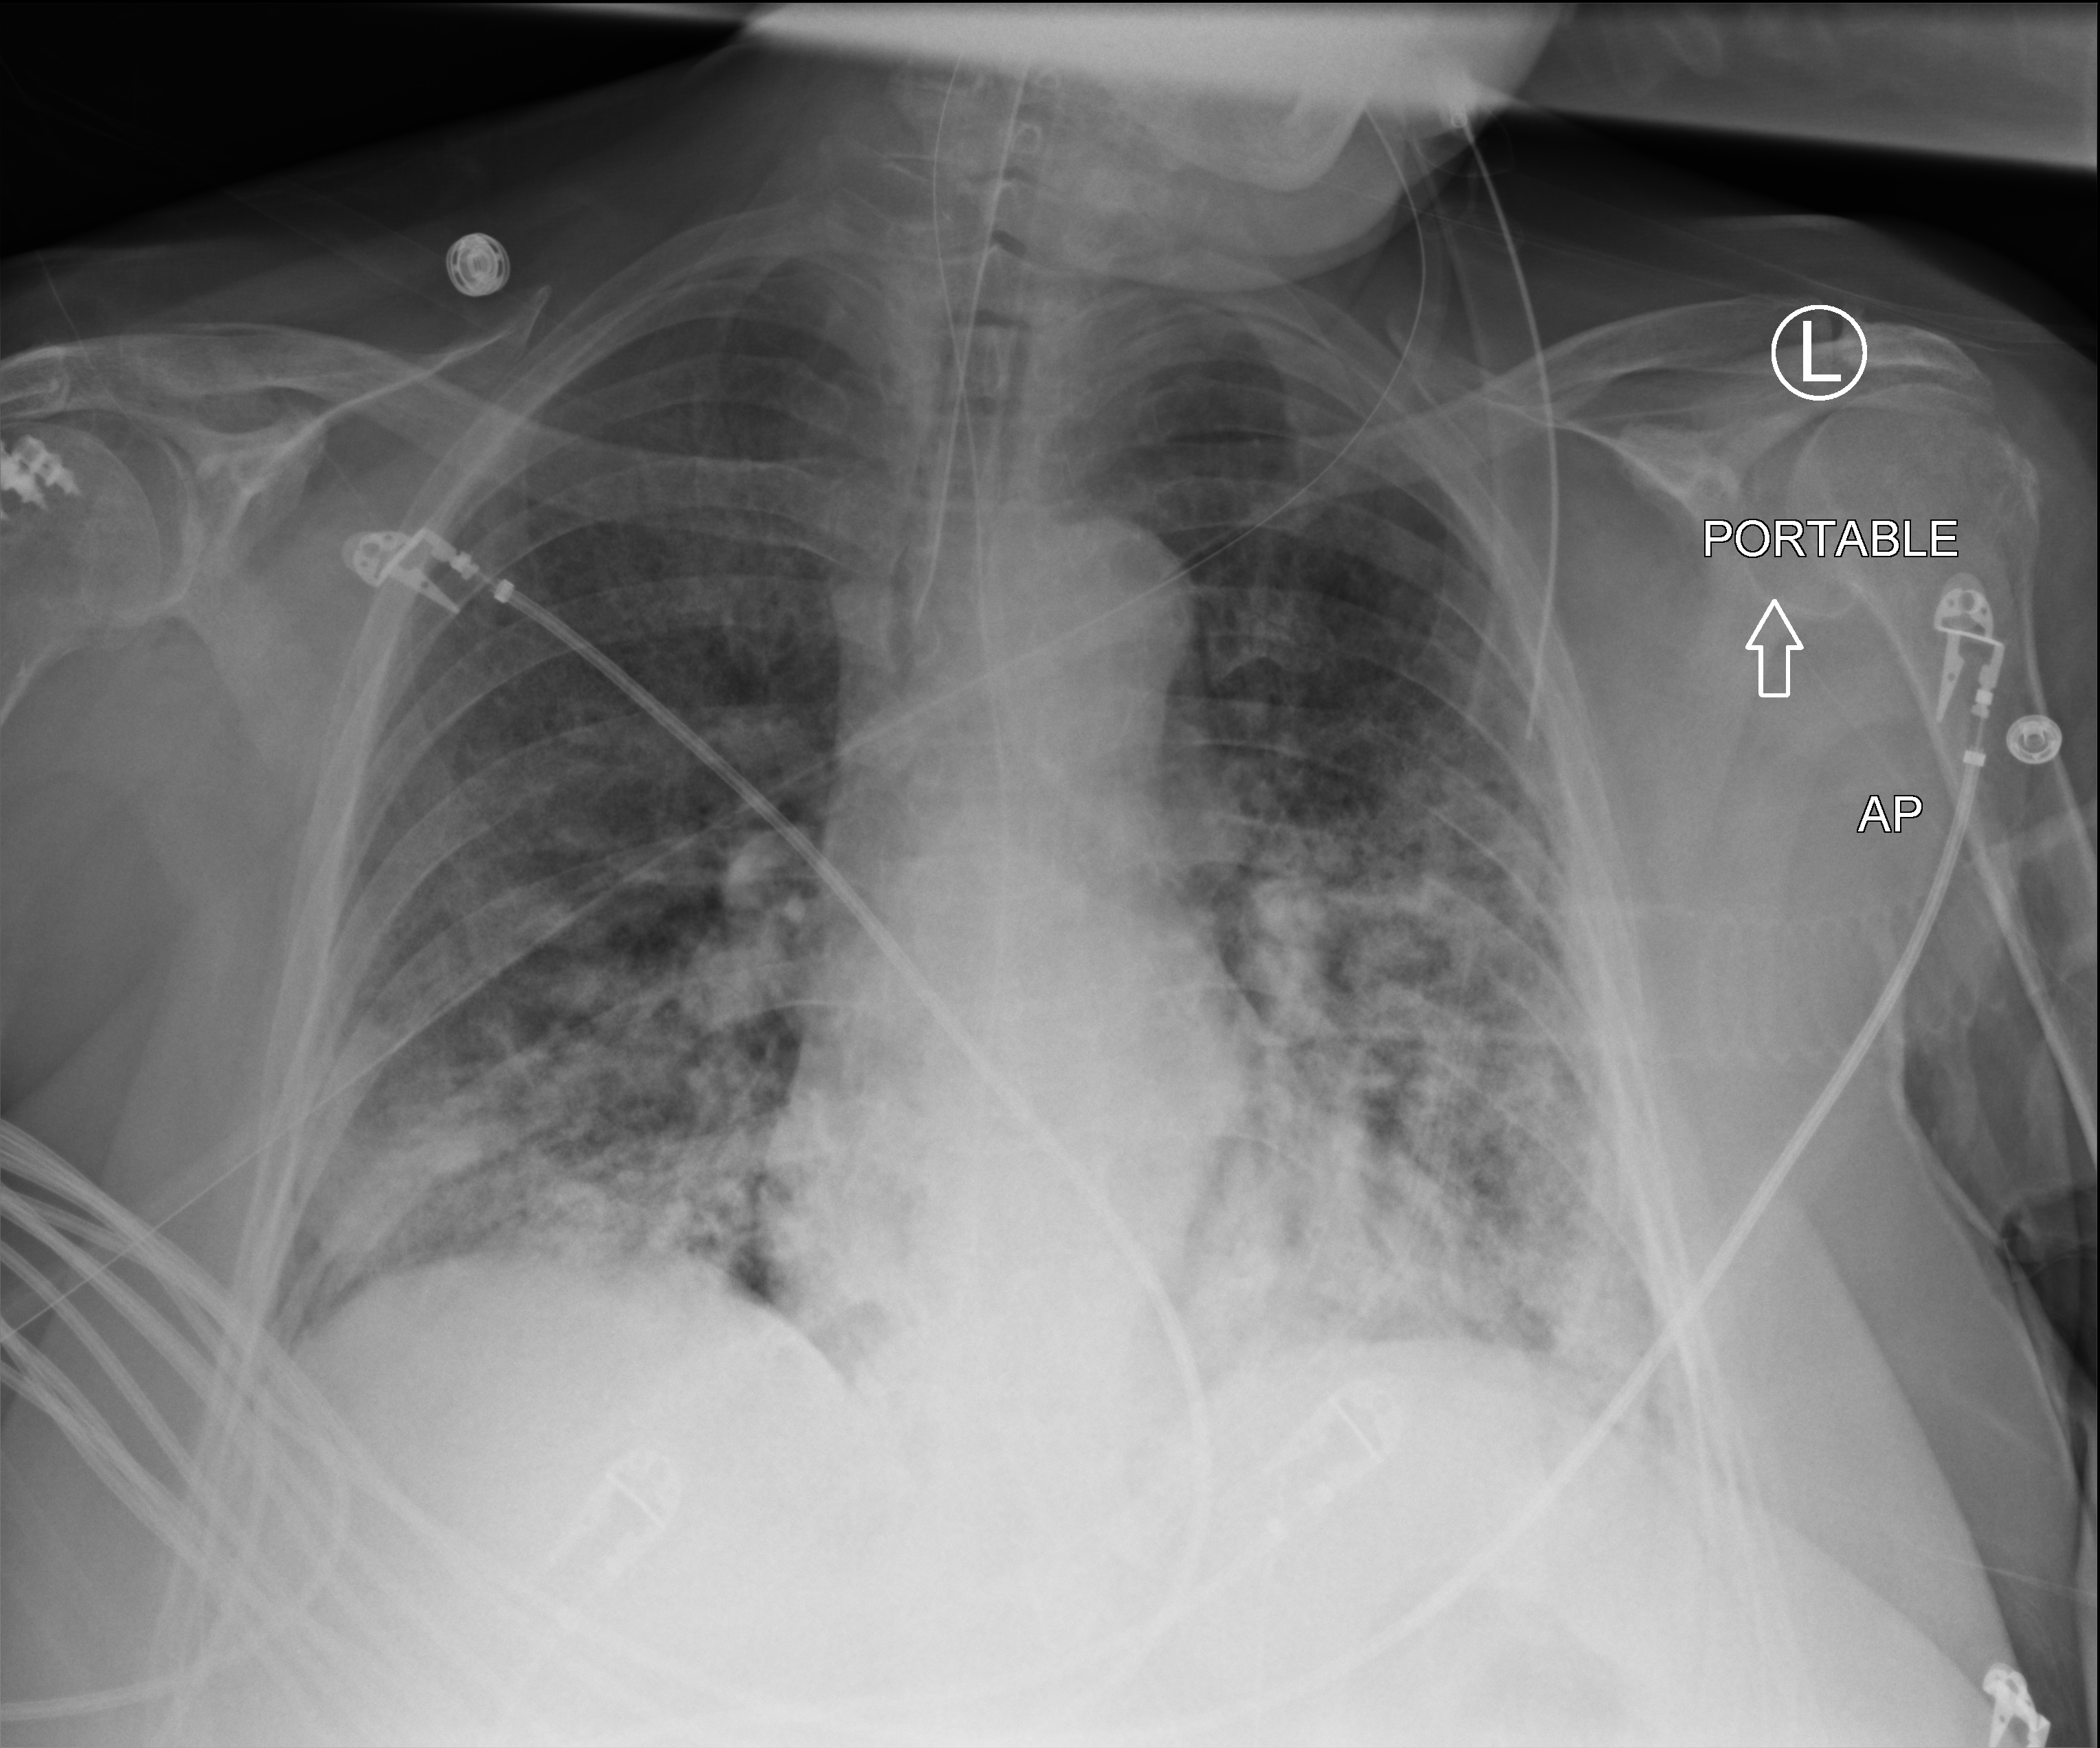
Portable chest radiograph, anteroposterior (AP) projection. Female patient hospitalised with COVID-19, age 60–74 years.
Admission-level facts for this patient (not findings on this image; timing relative to this image not recorded): mechanically ventilated during this hospital stay: yes.